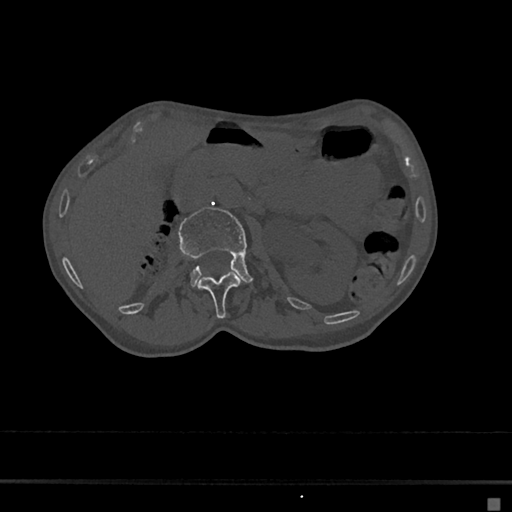
CT including the spine, one axial slice. Slice 44 of 797 in the series (ordered by position). Reconstruction kernel Br40s/3. Bone window (W 1800 / L 400 HU). 0.5 mm slice thickness. 512 × 512 image matrix, field of view 360 × 360 mm. Female patient, age 68 years. From the clinical record (not read from this slice): primary cancer: renal.
Annotated regions visible in this slice (semi-automatically segmented with operator editing):
- L1 vertebra: bounding box <197,272,240,319> (left, top, right, bottom; pixels)
- L2 vertebra: <179,207,252,286>